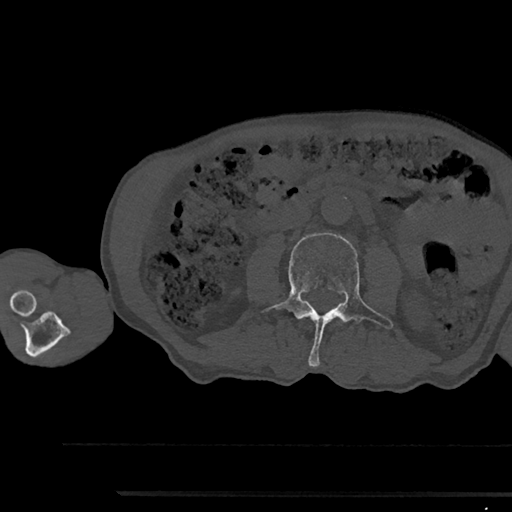
CT including the spine, one axial slice. Slice 494 of 797 in the series (ordered by position). Bone window (W 1800 / L 400 HU). 512 × 512 image matrix, field of view 367 × 367 mm. Male patient, age 79 years. Case-level facts recorded for this patient, not image findings: primary cancer: prostate.
Outlined on this slice (semi-automatic segmentation, software-assisted and operator-edited):
- L3 vertebra: bounding box [x1, y1, x2, y2] px = [260, 233, 393, 367]